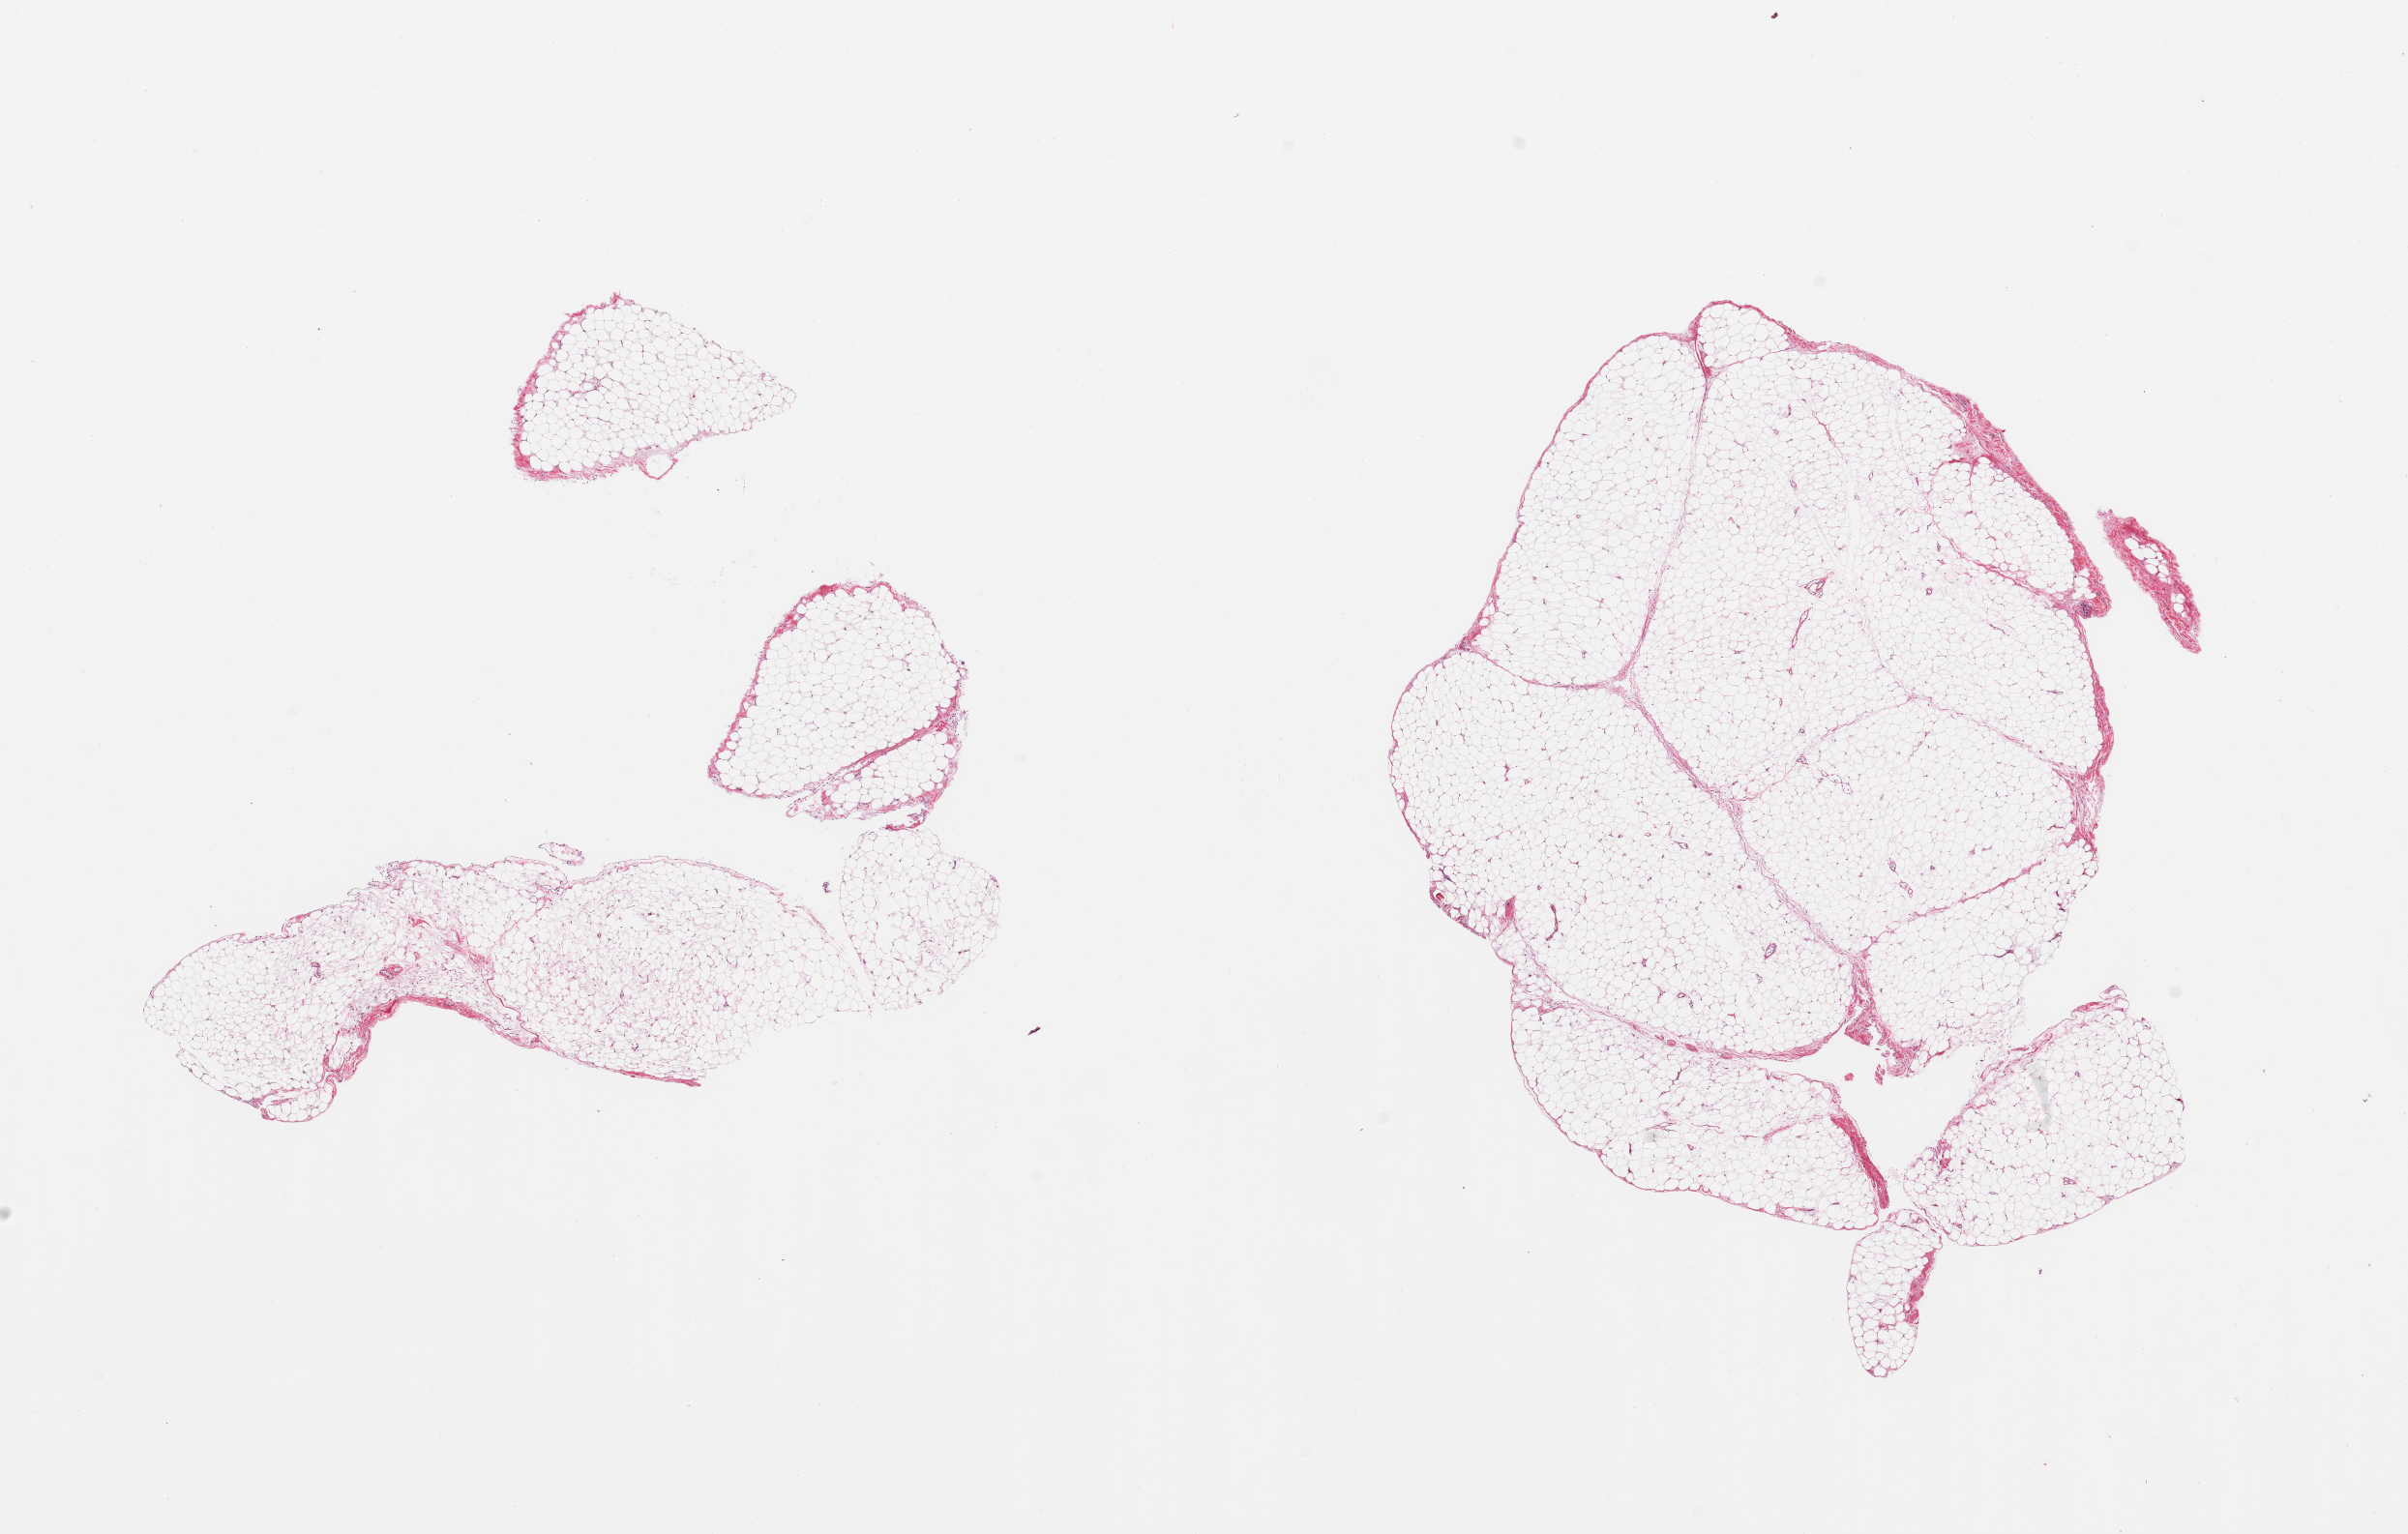
Digitized hematoxylin and eosin (H&E)-stained section — whole scanned area (about 19.7 x 12.5 mm) shown as a low-resolution overview; PAXgene-fixed, paraffin-embedded tissue; section of omentum (target tissue); donor tissue sample. Donor sex: male.
Pathologist's review note for this sample: 2 pieces, 1 fragmented.